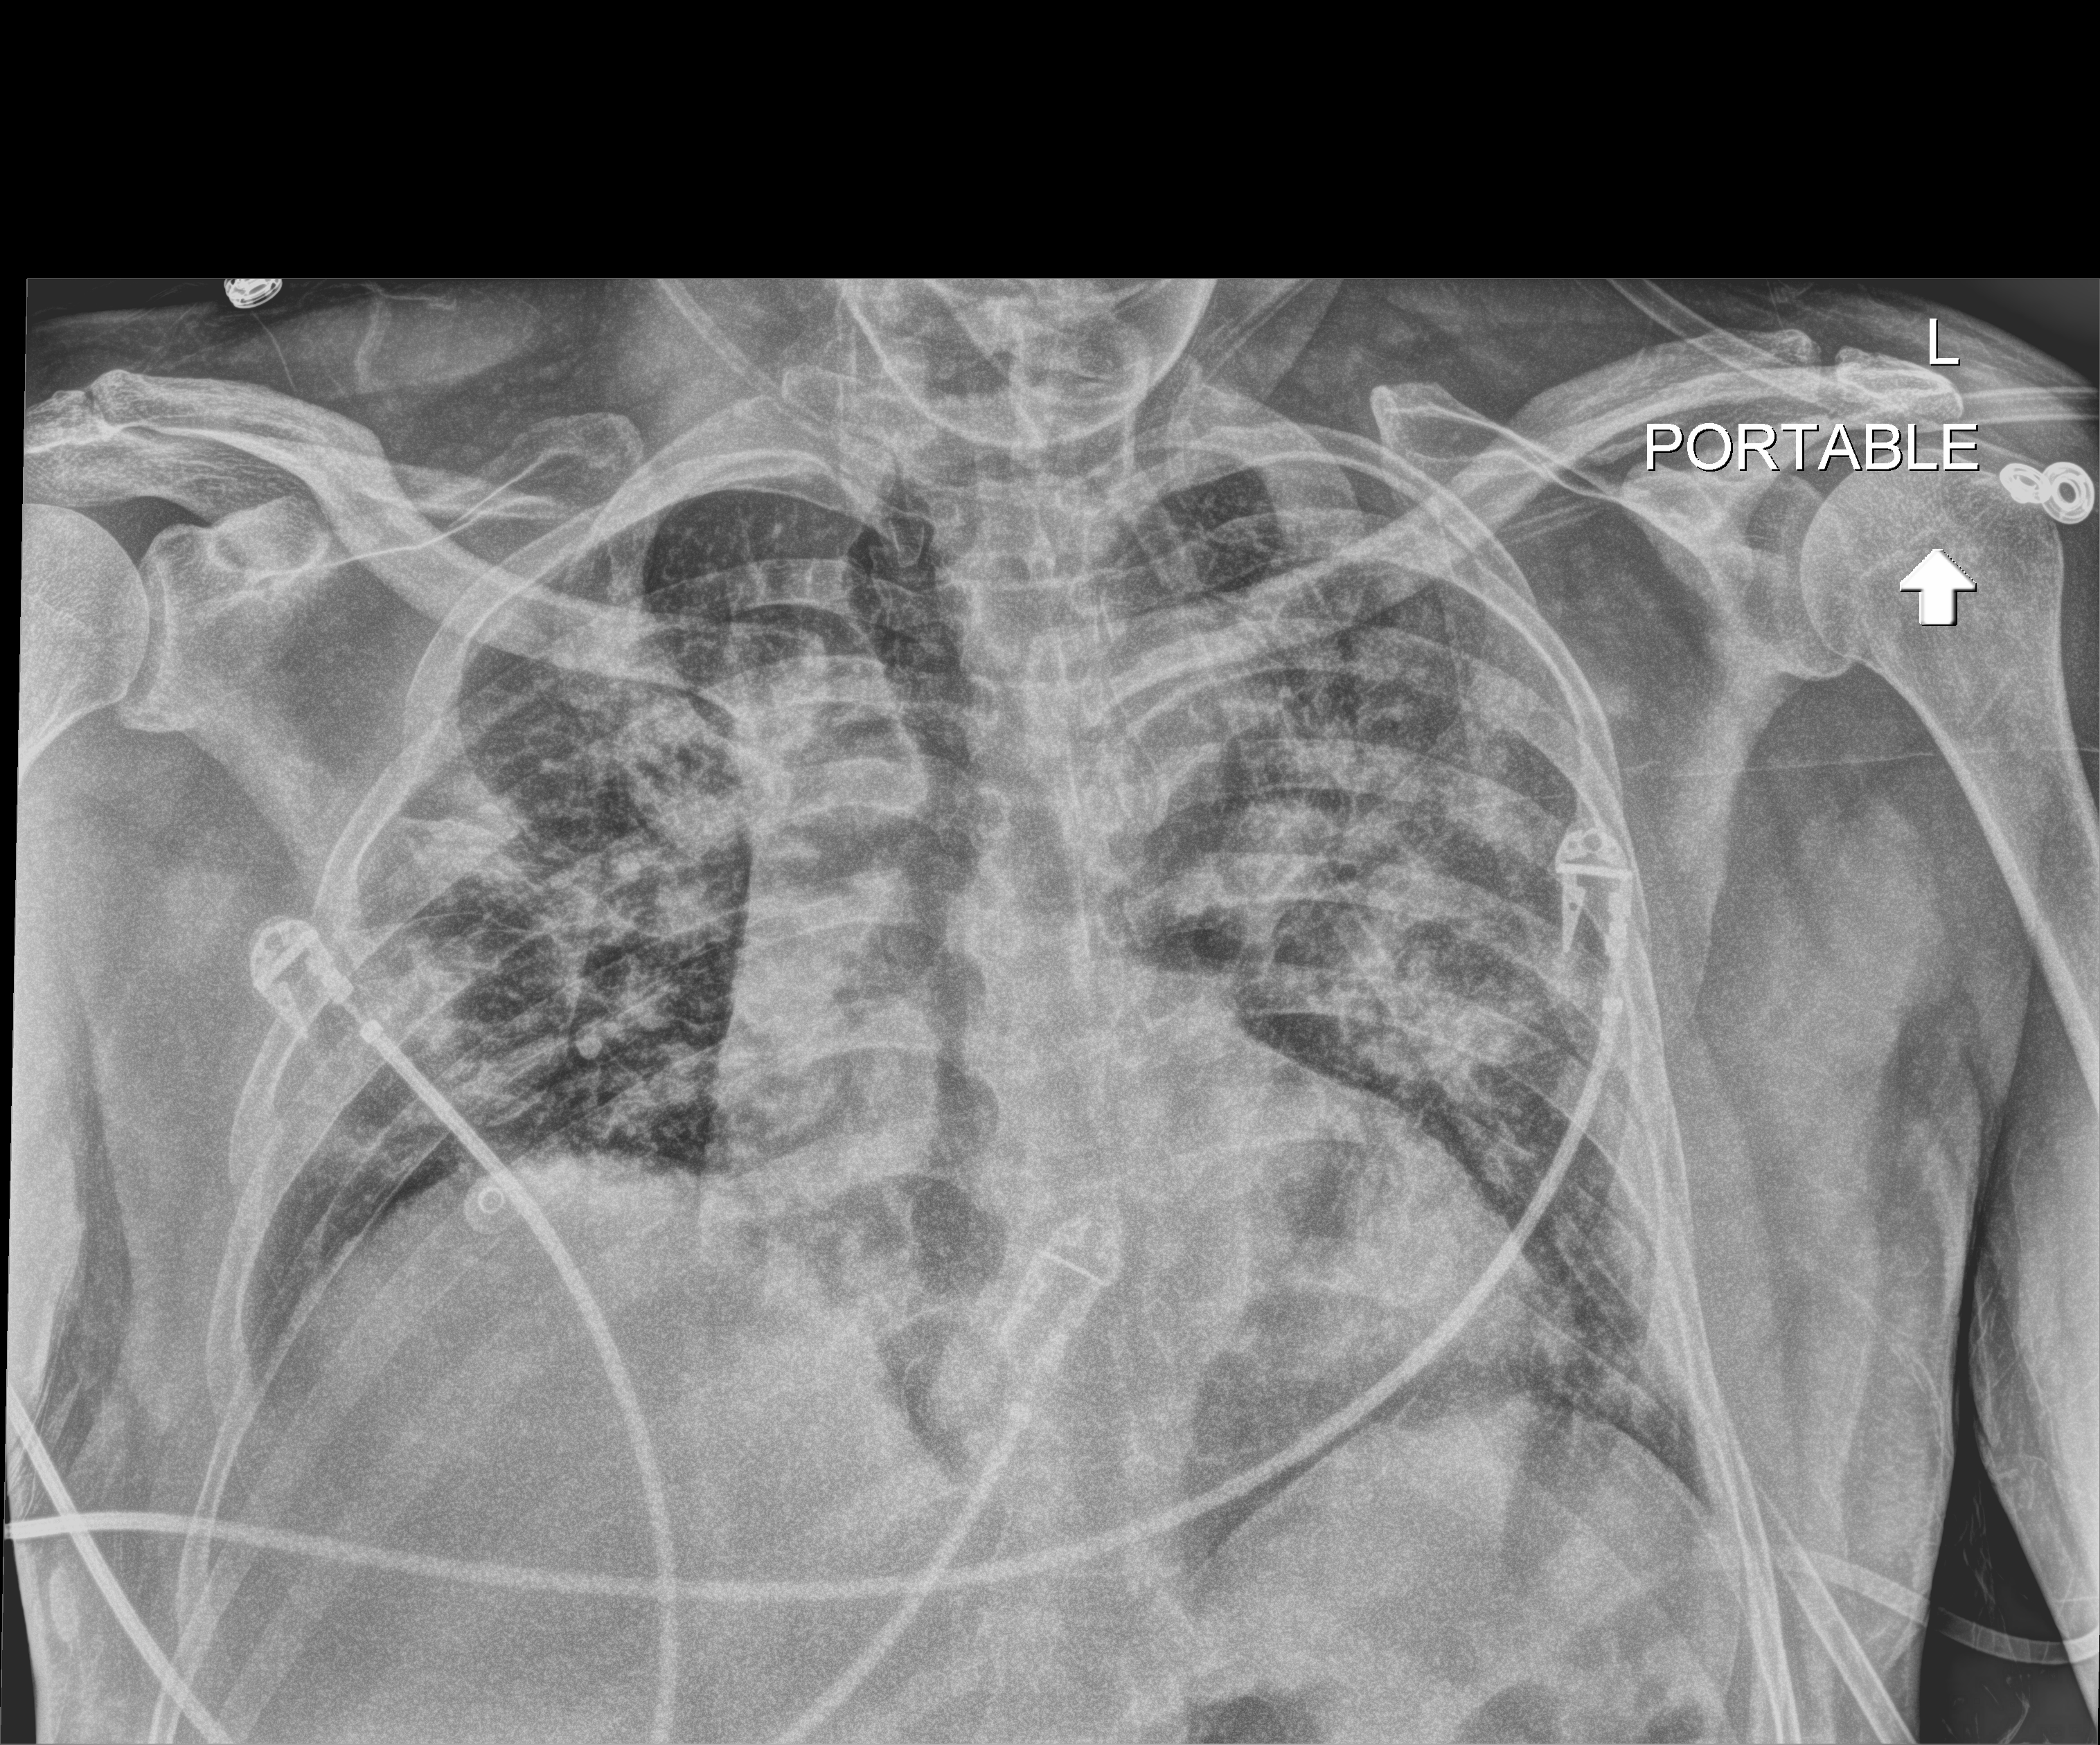
Portable chest radiograph. Patient hospitalised with COVID-19; male, aged 18–59 years.
Admission-level facts for this patient (not findings on this image; timing relative to this image not recorded):
- diabetes (admission record): no